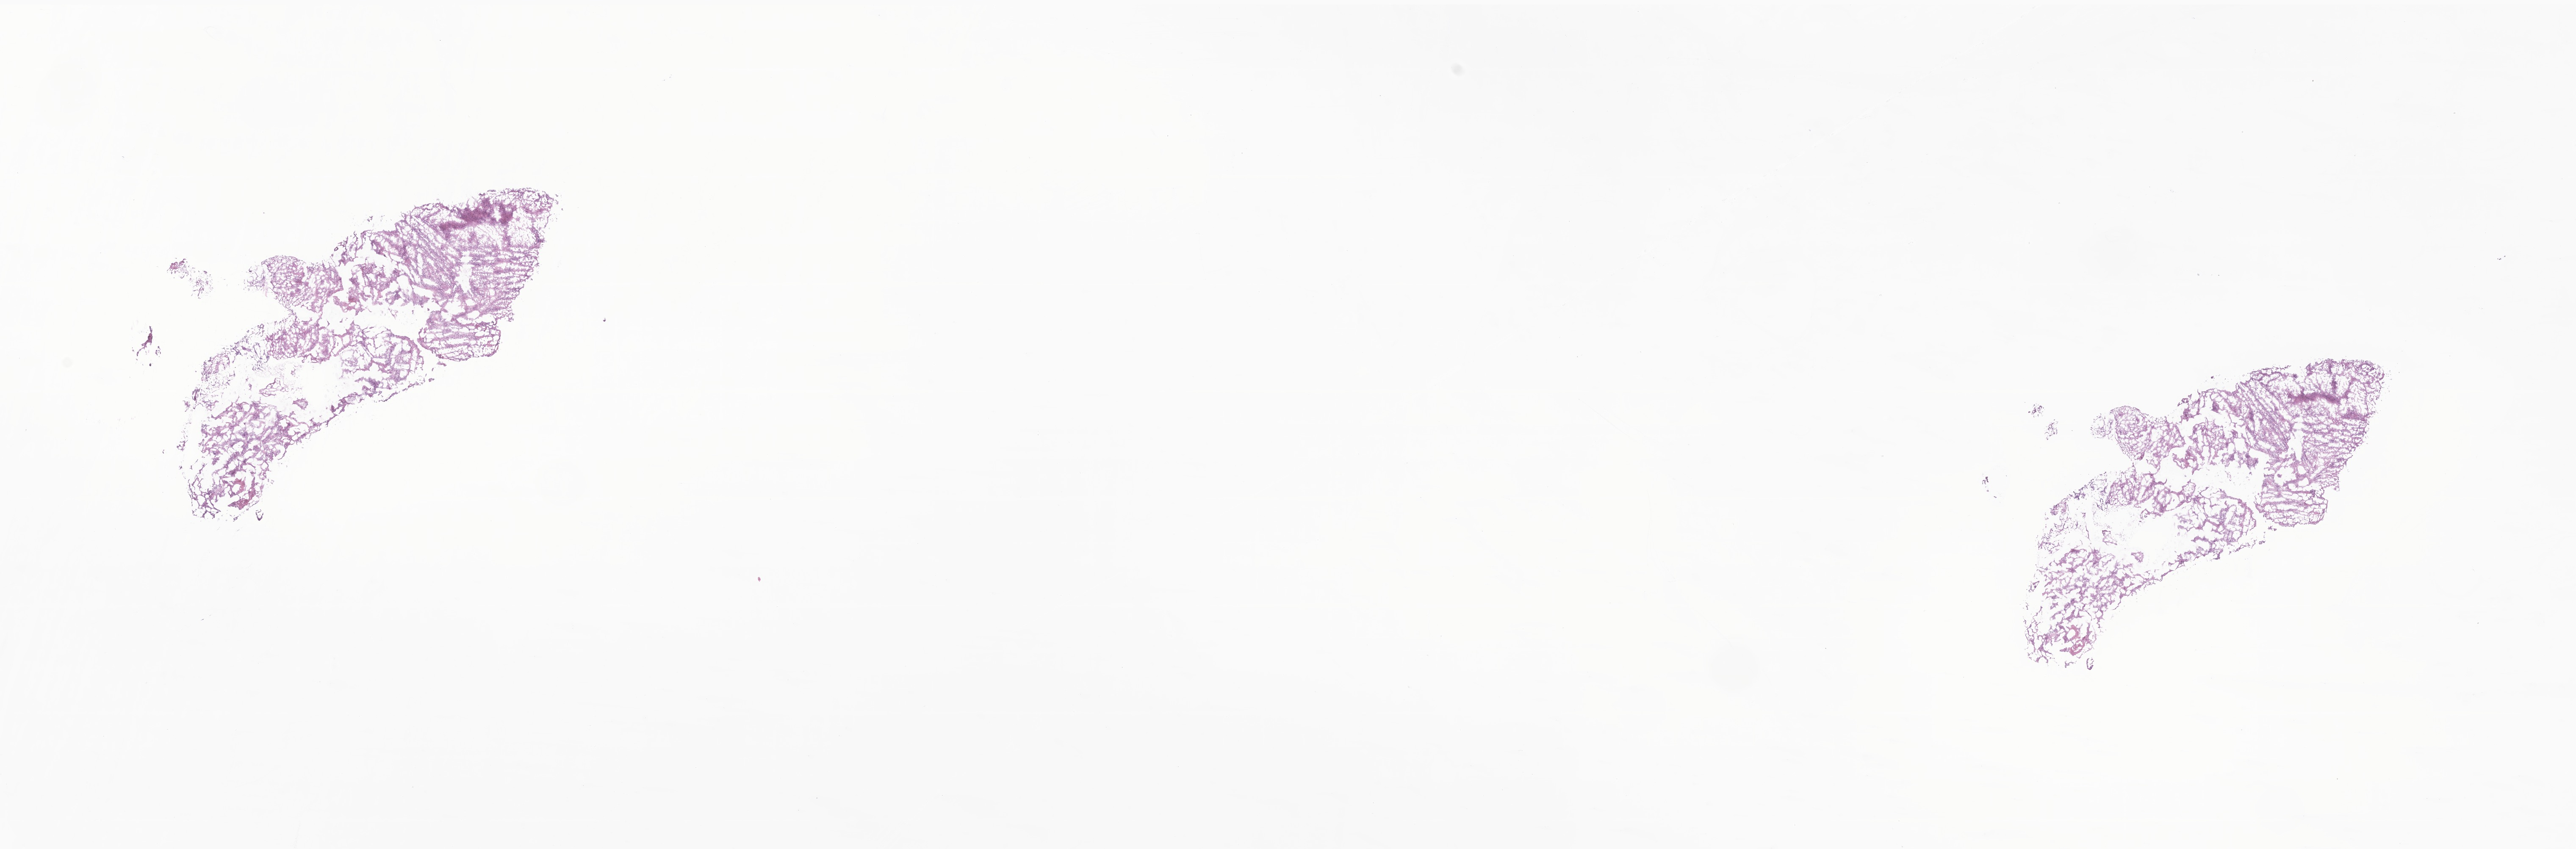
Haematoxylin and eosin whole-slide image of tumor tissue from the cerebellum, whole scanned area (about 25.6 x 8.5 mm) shown as a low-resolution overview; cryosection (OCT / tissue freezing medium). Female patient, age 100 months (8 years 4 months).
Diagnosis: Neoplasm, uncertain whether benign or malignant.